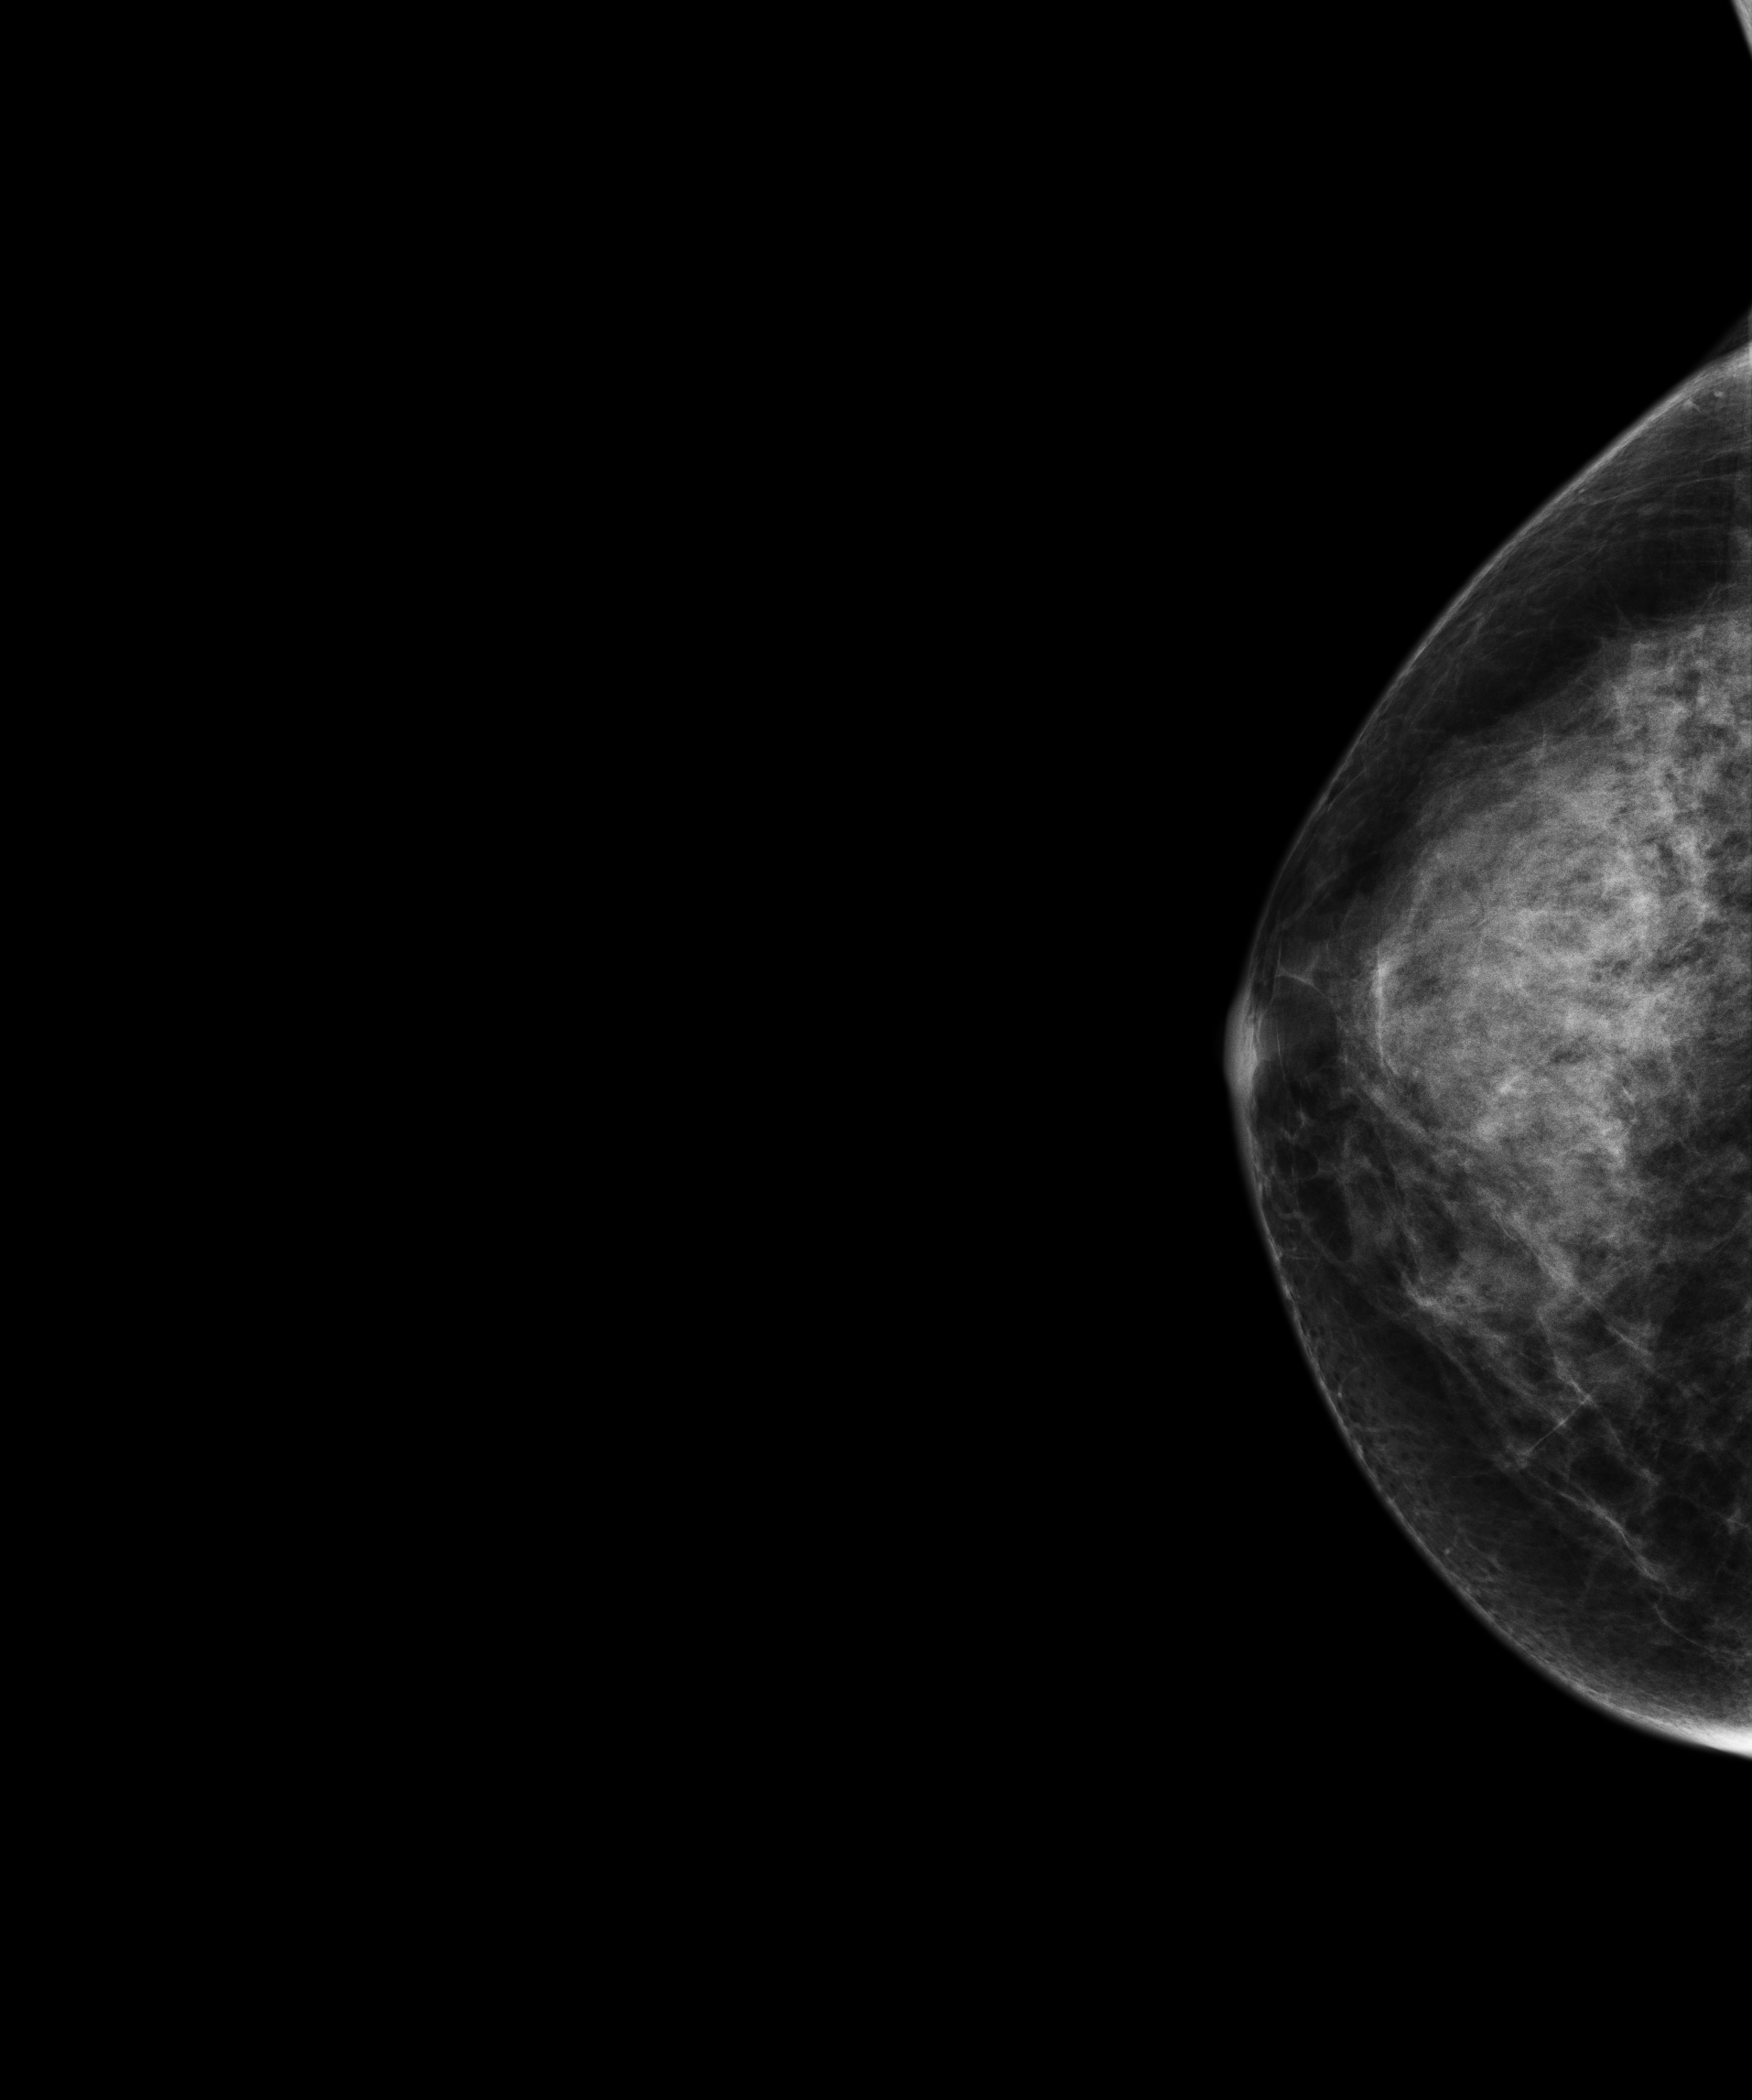
Screening examination; compressed breast thickness 55 mm; system: Senographe Essential ADS_56.21.3. Patient: female, 56 years.
Image type: full-field digital mammogram. Breast: right. Projection: cranio-caudal projection.